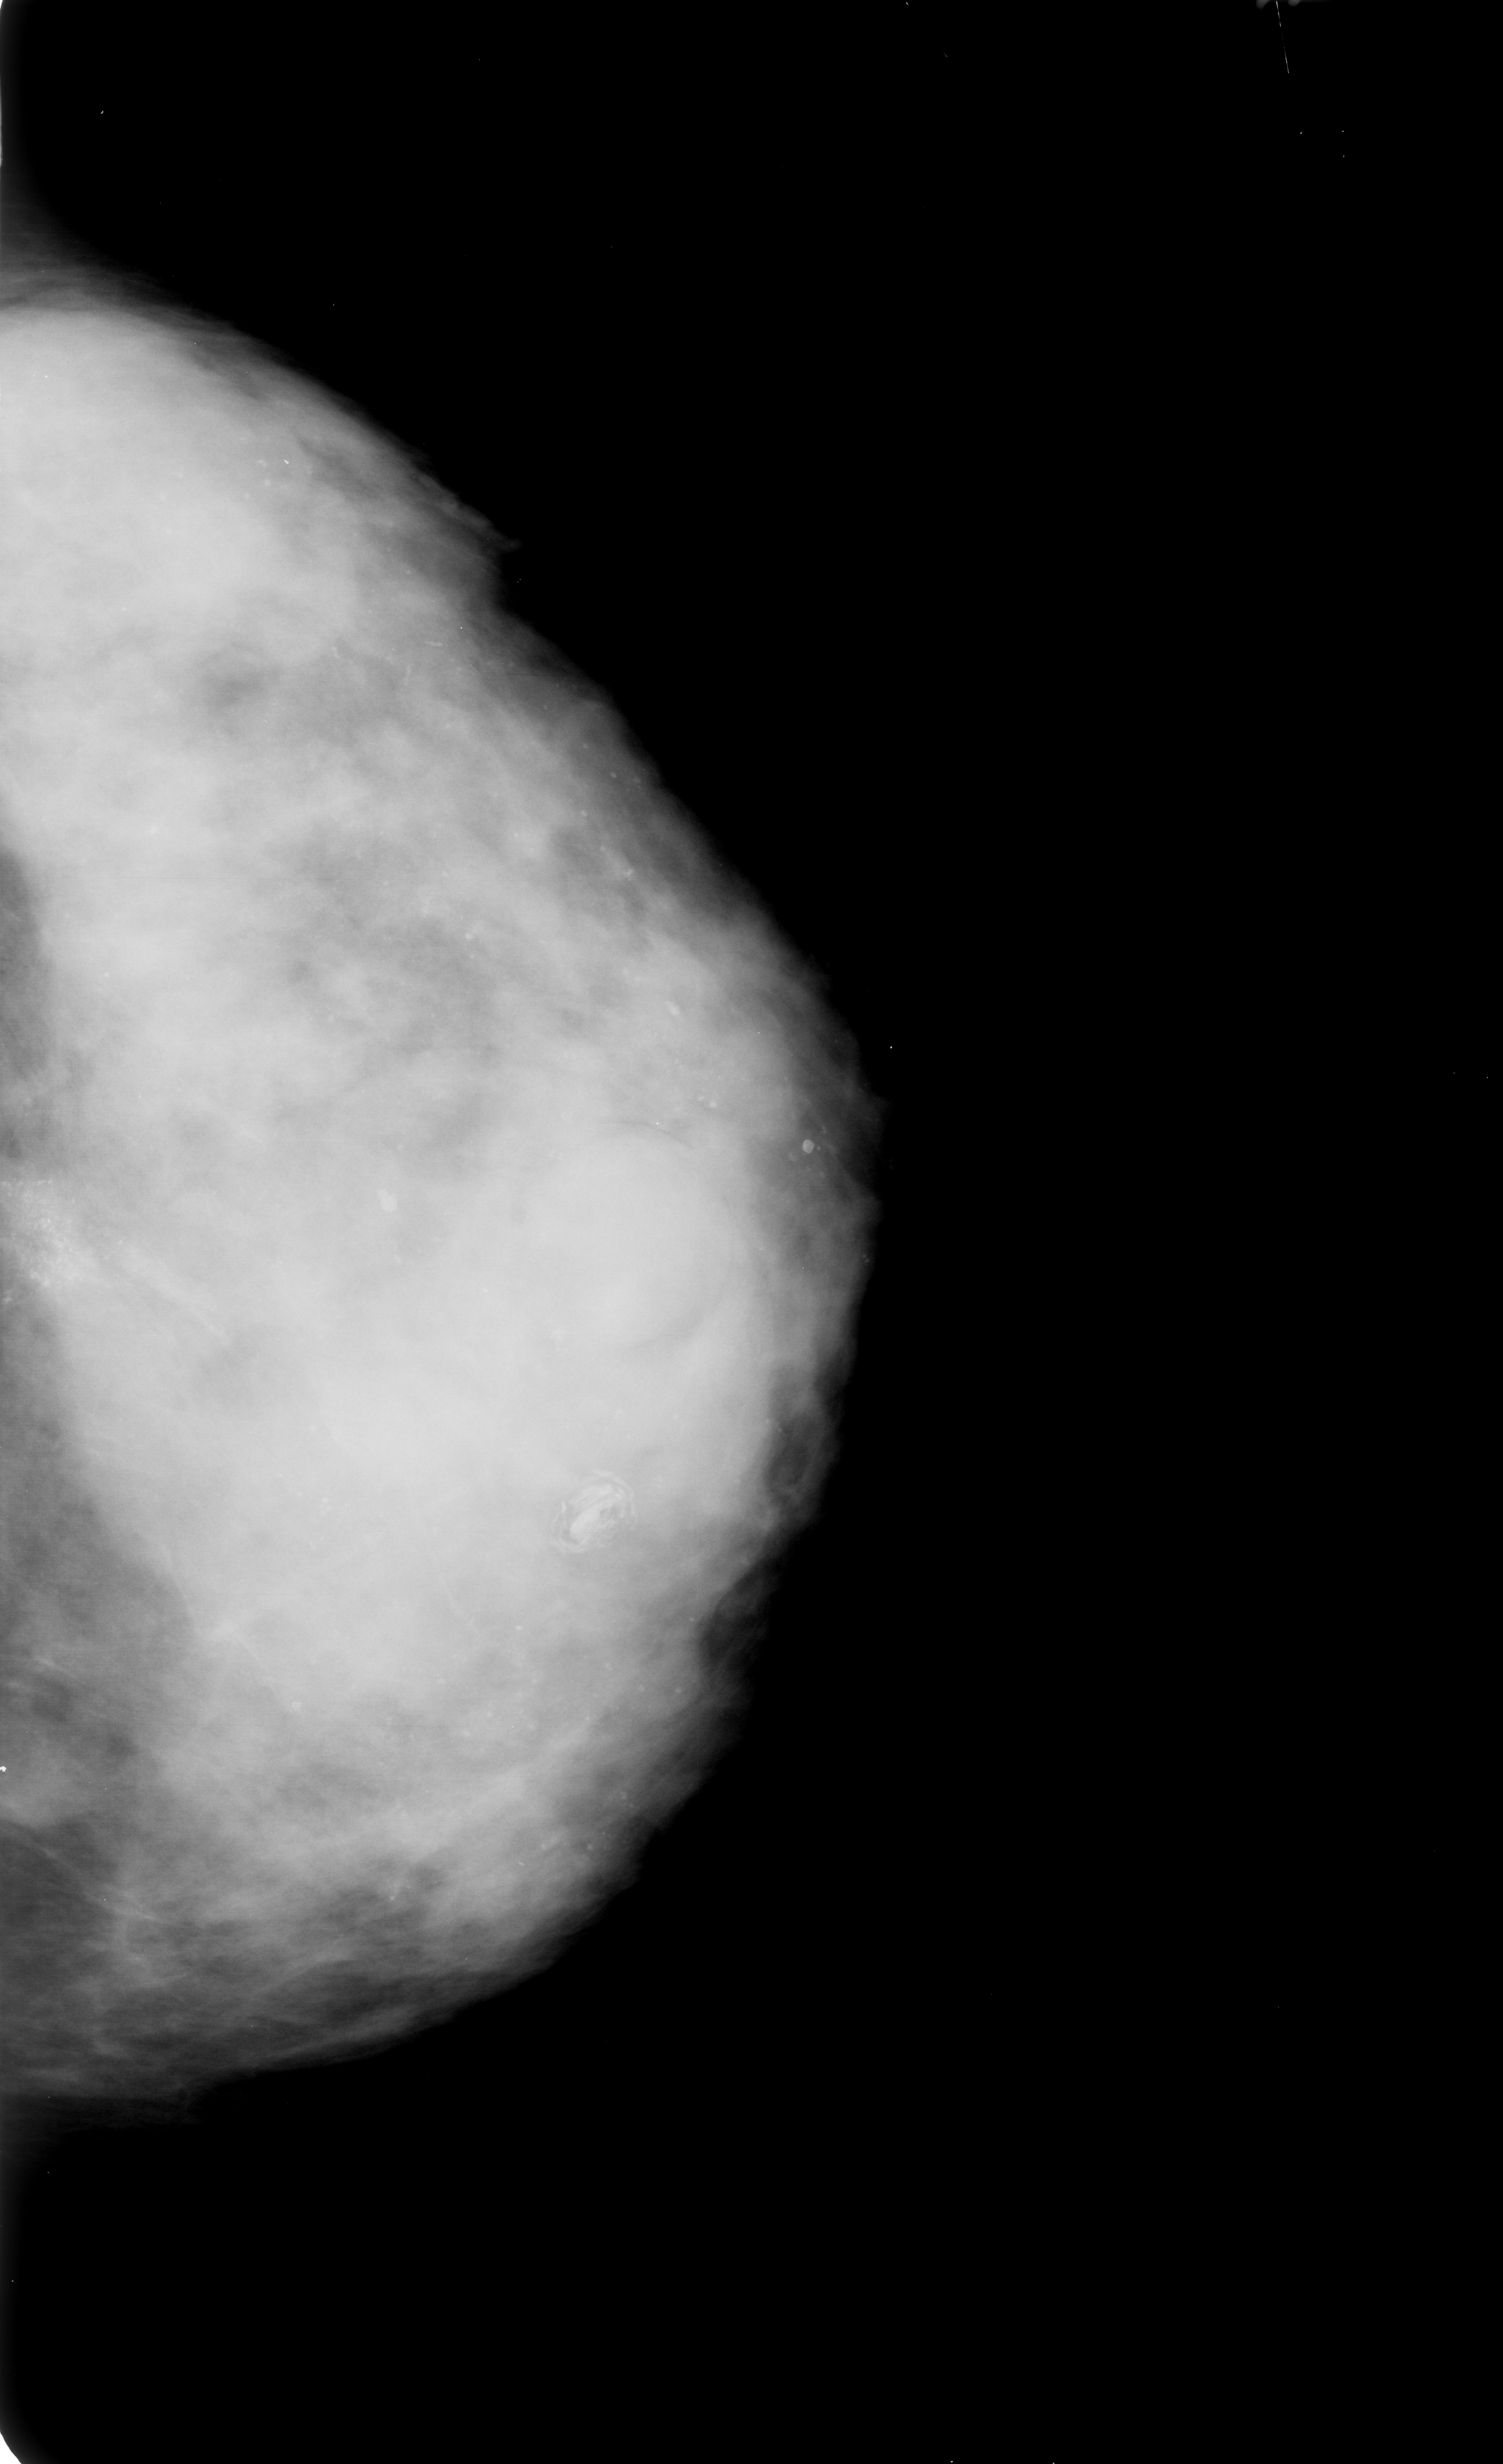
Digitized screen-film mammogram; left breast; CC view; breast composition: extremely dense (BI-RADS density category 4 of 4).
Radiologist-marked abnormalities on this image: mass, shape round, margins circumscribed; BI-RADS assessment category 3; subtlety rating 3 on a 1 (subtle) to 5 (obvious) scale; pathology (as recorded): benign.